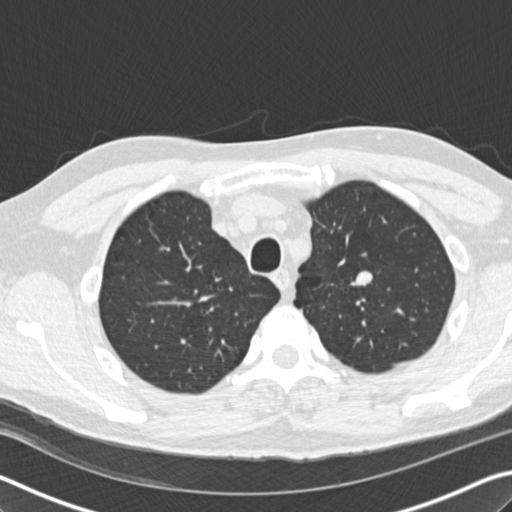
Axial slice from a low-dose chest CT screening exam; first (baseline) screen; lung window (W 1500 / L -600 HU); standard (soft-tissue) reconstruction kernel (B30f); slice 41 of 208 in the series; 512 × 512 image matrix, field of view 340 × 340 mm. Male, age 56 years at enrolment. Current smoker at enrolment.
Expert-annotated lung lesion, box from (x=338, y=261) to (x=390, y=302) px. The exam's reader record, not a measurement of the box and not confirmed to be the same lesion: non-calcified nodule or mass ≥4 mm, left upper lobe, 12 × 10 mm, smooth margins, soft tissue attenuation. Participant outcome: lung cancer diagnosed 814 days after this screen — neuroendocrine carcinoma, NOS, left upper lobe, well differentiated (G1), stage IA (AJCC 6th edition), 20 mm at pathology.